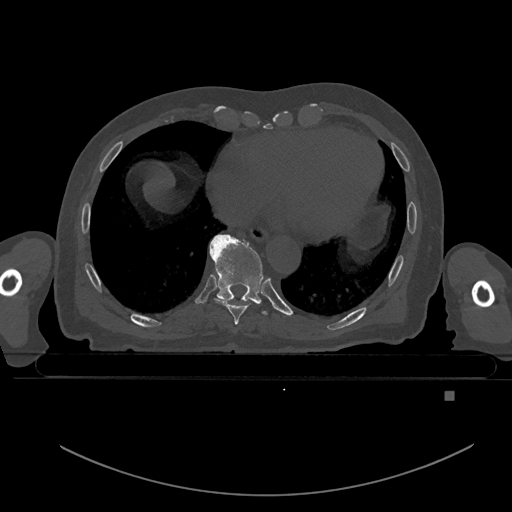
CT including the spine, one axial slice; slice 171 of 969 in the series (ordered by position); bone window (W 1800 / L 400 HU); 0.5 mm slice thickness; 512 × 512 image matrix, field of view 456 × 456 mm. Patient: male, 82 years. From the clinical record (not read from this slice): primary cancer: prostate; vertebrae with lytic lesions (as recorded): T11, T9, T8, T2.
Annotated regions visible in this slice (semi-automatic segmentation, software-assisted and operator-edited):
- T8 vertebra: bounding box [x1, y1, x2, y2] px = [214, 297, 252, 325]
- T9 vertebra: [209, 234, 268, 314]